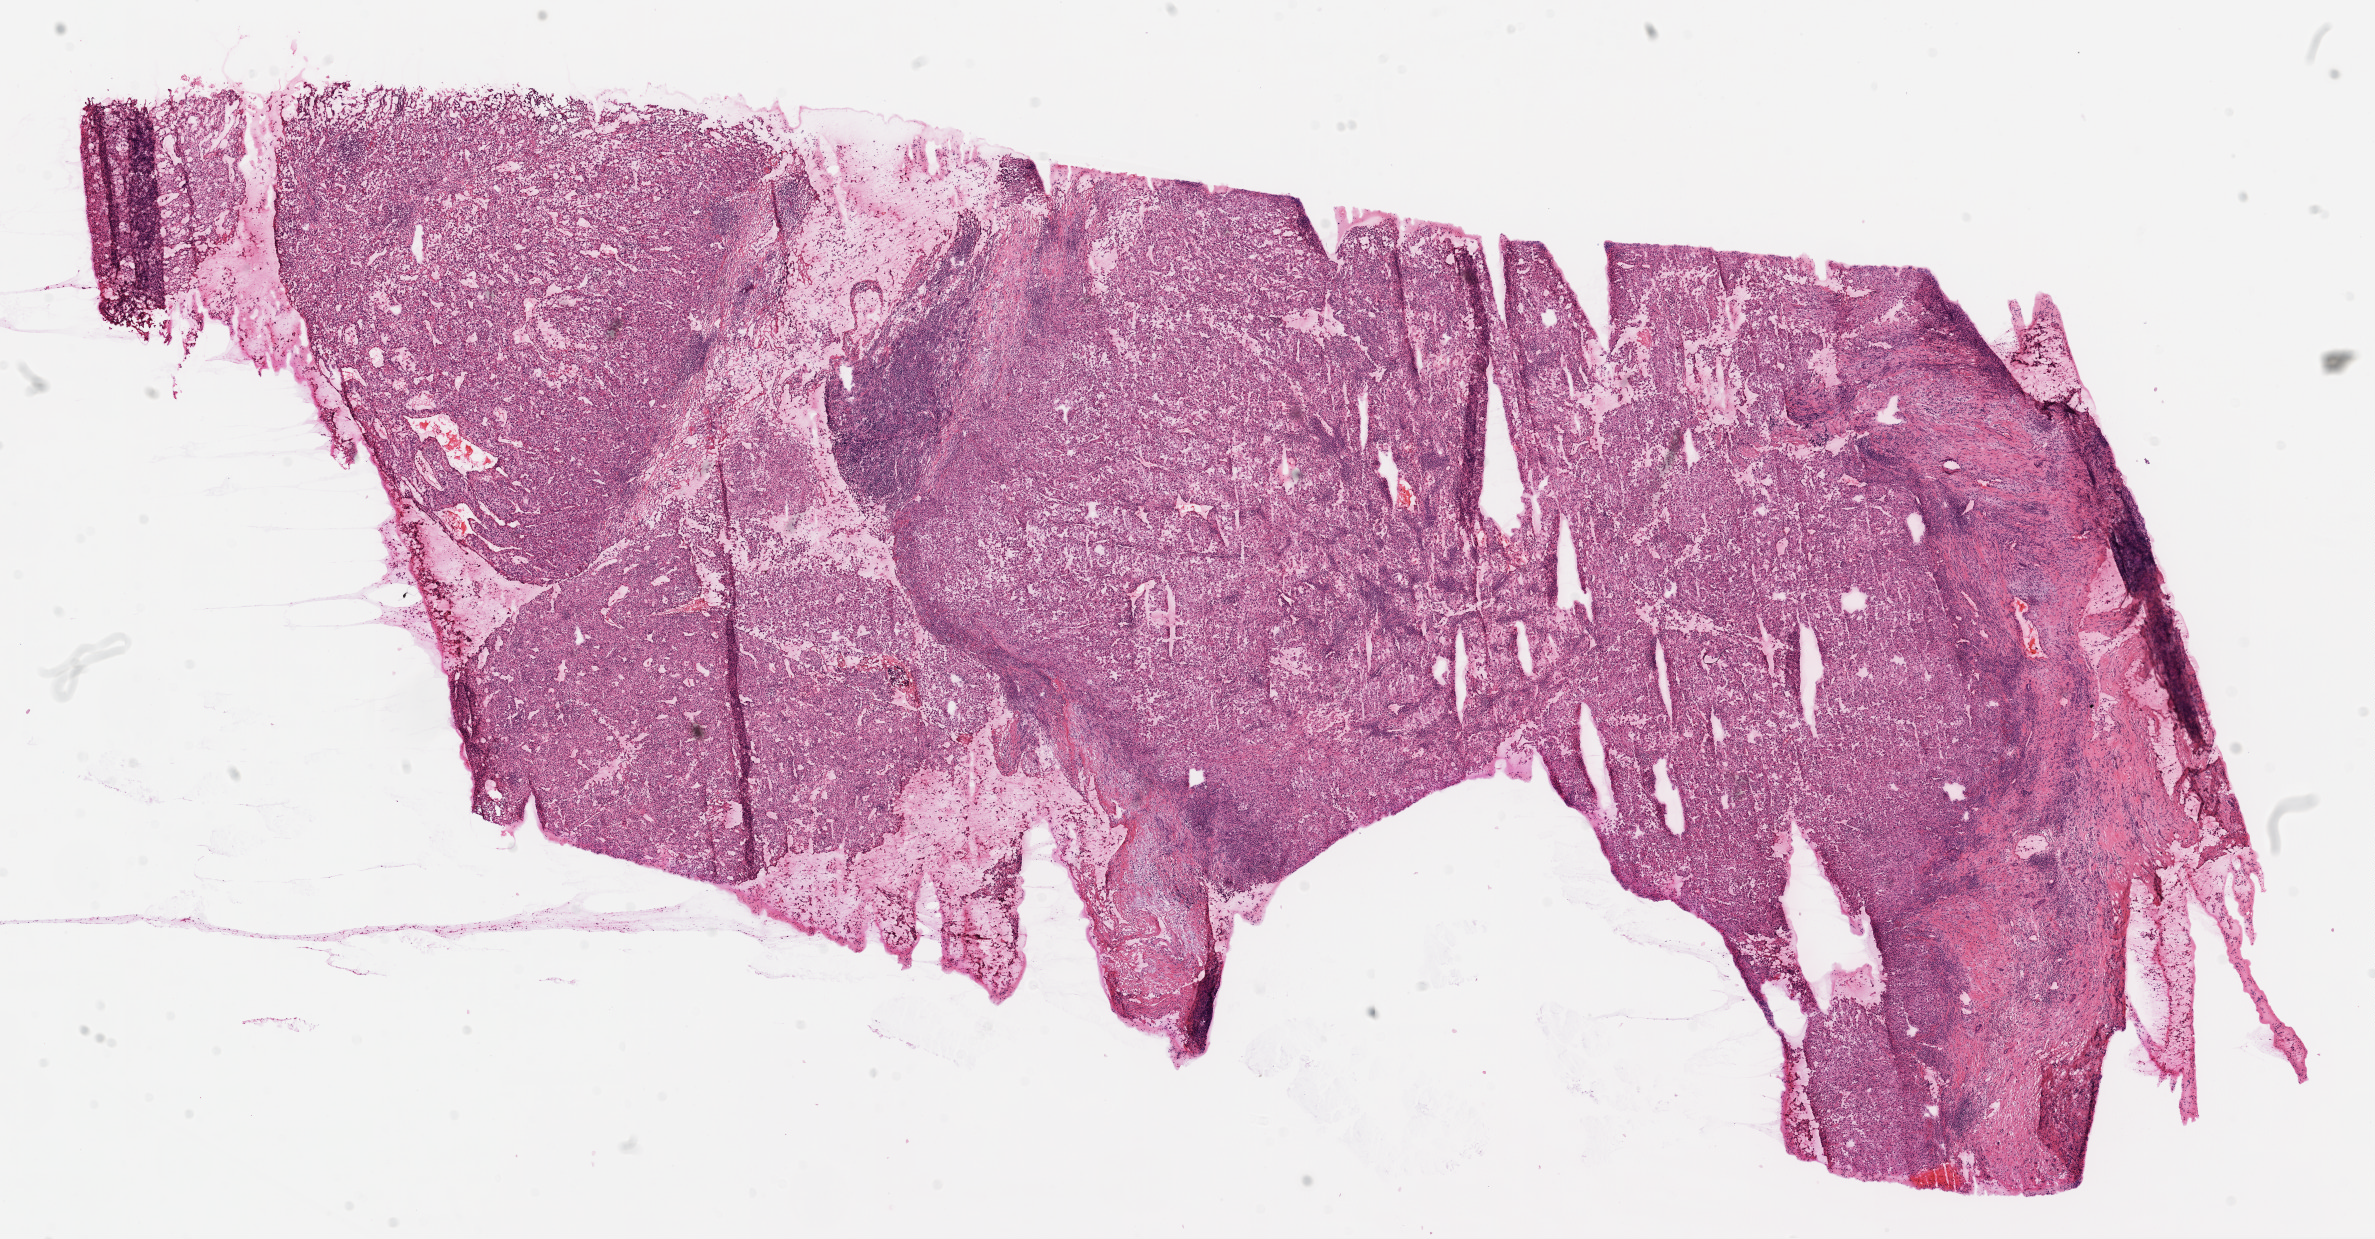
Hematoxylin and eosin (H&E) stained whole-slide image, whole scanned area (about 19.1 x 9.9 mm, from a 20x scan) shown as a low-resolution overview. Frozen section from the top of the tissue portion. Sample: primary tumour, kidney. Patient: female, age at initial diagnosis 52 years. Composition of this section per pathologist review: tumour cells 95%, tumour nuclei 85%.
Diagnosis: Clear cell adenocarcinoma, NOS.